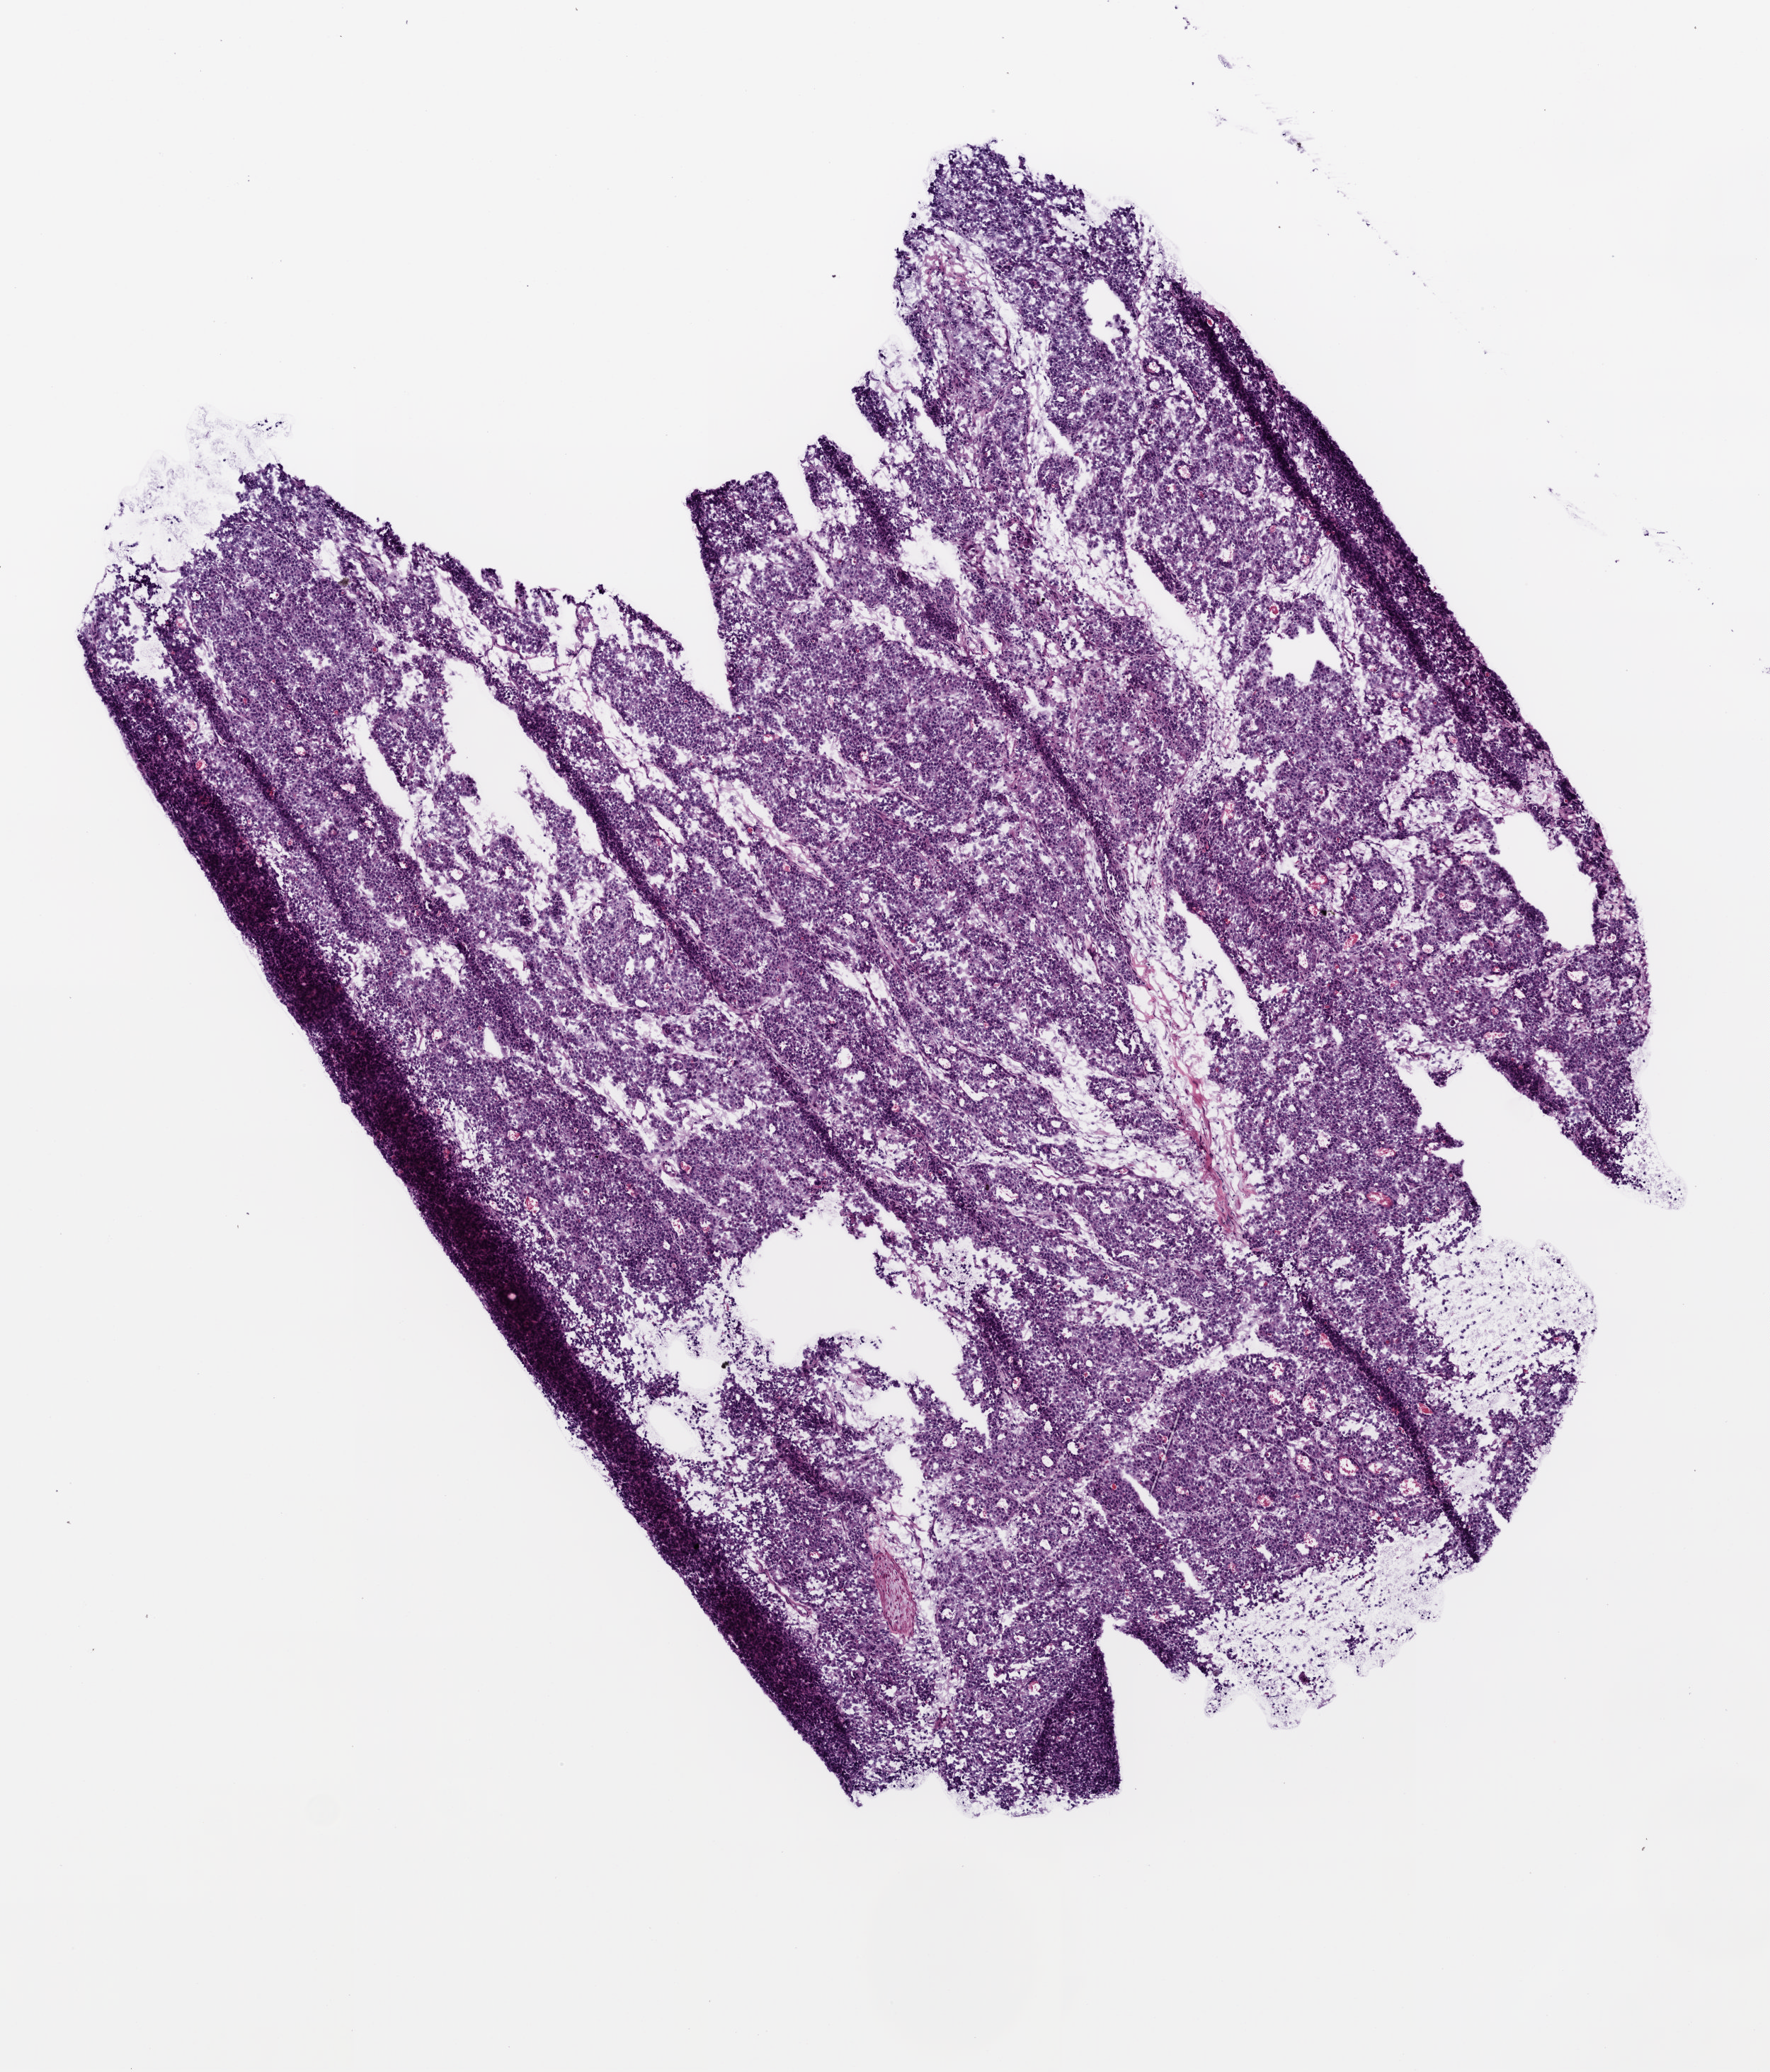
Hematoxylin and eosin (H&E) stained whole-slide image, a low-resolution overview of the entire scanned area, about 5.0 x 5.9 mm (slide scanned at 20x), frozen section, stomach, primary tumour sample. Male, age 68 years at initial diagnosis. Histologic grade: G2 (moderately differentiated). Composition of this section per pathologist review: tumour cells 92%, tumour nuclei 80%, normal cells 0%, stromal cells 5%, necrosis 3%.
• lymph nodes positive (case pathology): 0 of 30 examined
• AJCC pathologic stage: IA (5th edition)
• diagnosis: Adenocarcinoma, intestinal type (body of stomach)
• TNM: T1 N0 M0